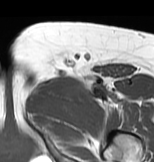
MRI of an extremity soft-tissue mass, one axial slice; slice 48 of 83 in the series (ordered by position); MR volume resampled by the dataset authors to the PET/CT grid (not the native acquisition matrix); 3.27 mm slice thickness; 154 × 162 image matrix, field of view 150 × 158 mm. Female patient. Case-level facts recorded for this patient, not image findings: histological type: myxofibrosarcoma; grade: intermediate; site of the primary tumour: left thigh.
Annotated regions visible in this slice (expert contour drawn on MRI and transferred to this co-registered scan by the dataset authors):
- gross tumour volume including surrounding oedema: bounding box <26,73,123,115> (left, top, right, bottom; pixels)